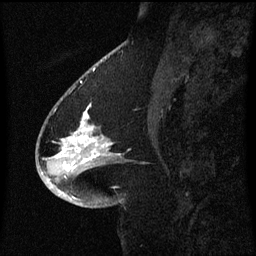
Breast MRI (dynamic contrast-enhanced), one sagittal slice. Position 26 of 60 along the scan axis. Dynamic contrast-enhanced series, image 2 of 3 at this slice position (ordered by acquisition). 1.5 T. TE 4.2 ms, TR 8.4 ms. 256 × 256 image matrix, field of view 200 × 200 mm. Patient: female, 54 years. From the clinical record (not read from this slice): setting: breast cancer imaged before/during neoadjuvant chemotherapy; receptor status: HR-positive, HER2-negative.
Annotated regions visible in this slice (semi-automatic segmentation, software-assisted and operator-edited):
- analysis volume of interest (the breast-tissue region the enhancement analysis was run in; not a lesion): bounding box [x1, y1, x2, y2] px = [47, 100, 121, 171]
- tumour enhancement mask (voxels above the 70 % enhancement threshold inside the analysis volume of interest): [63, 110, 110, 147]